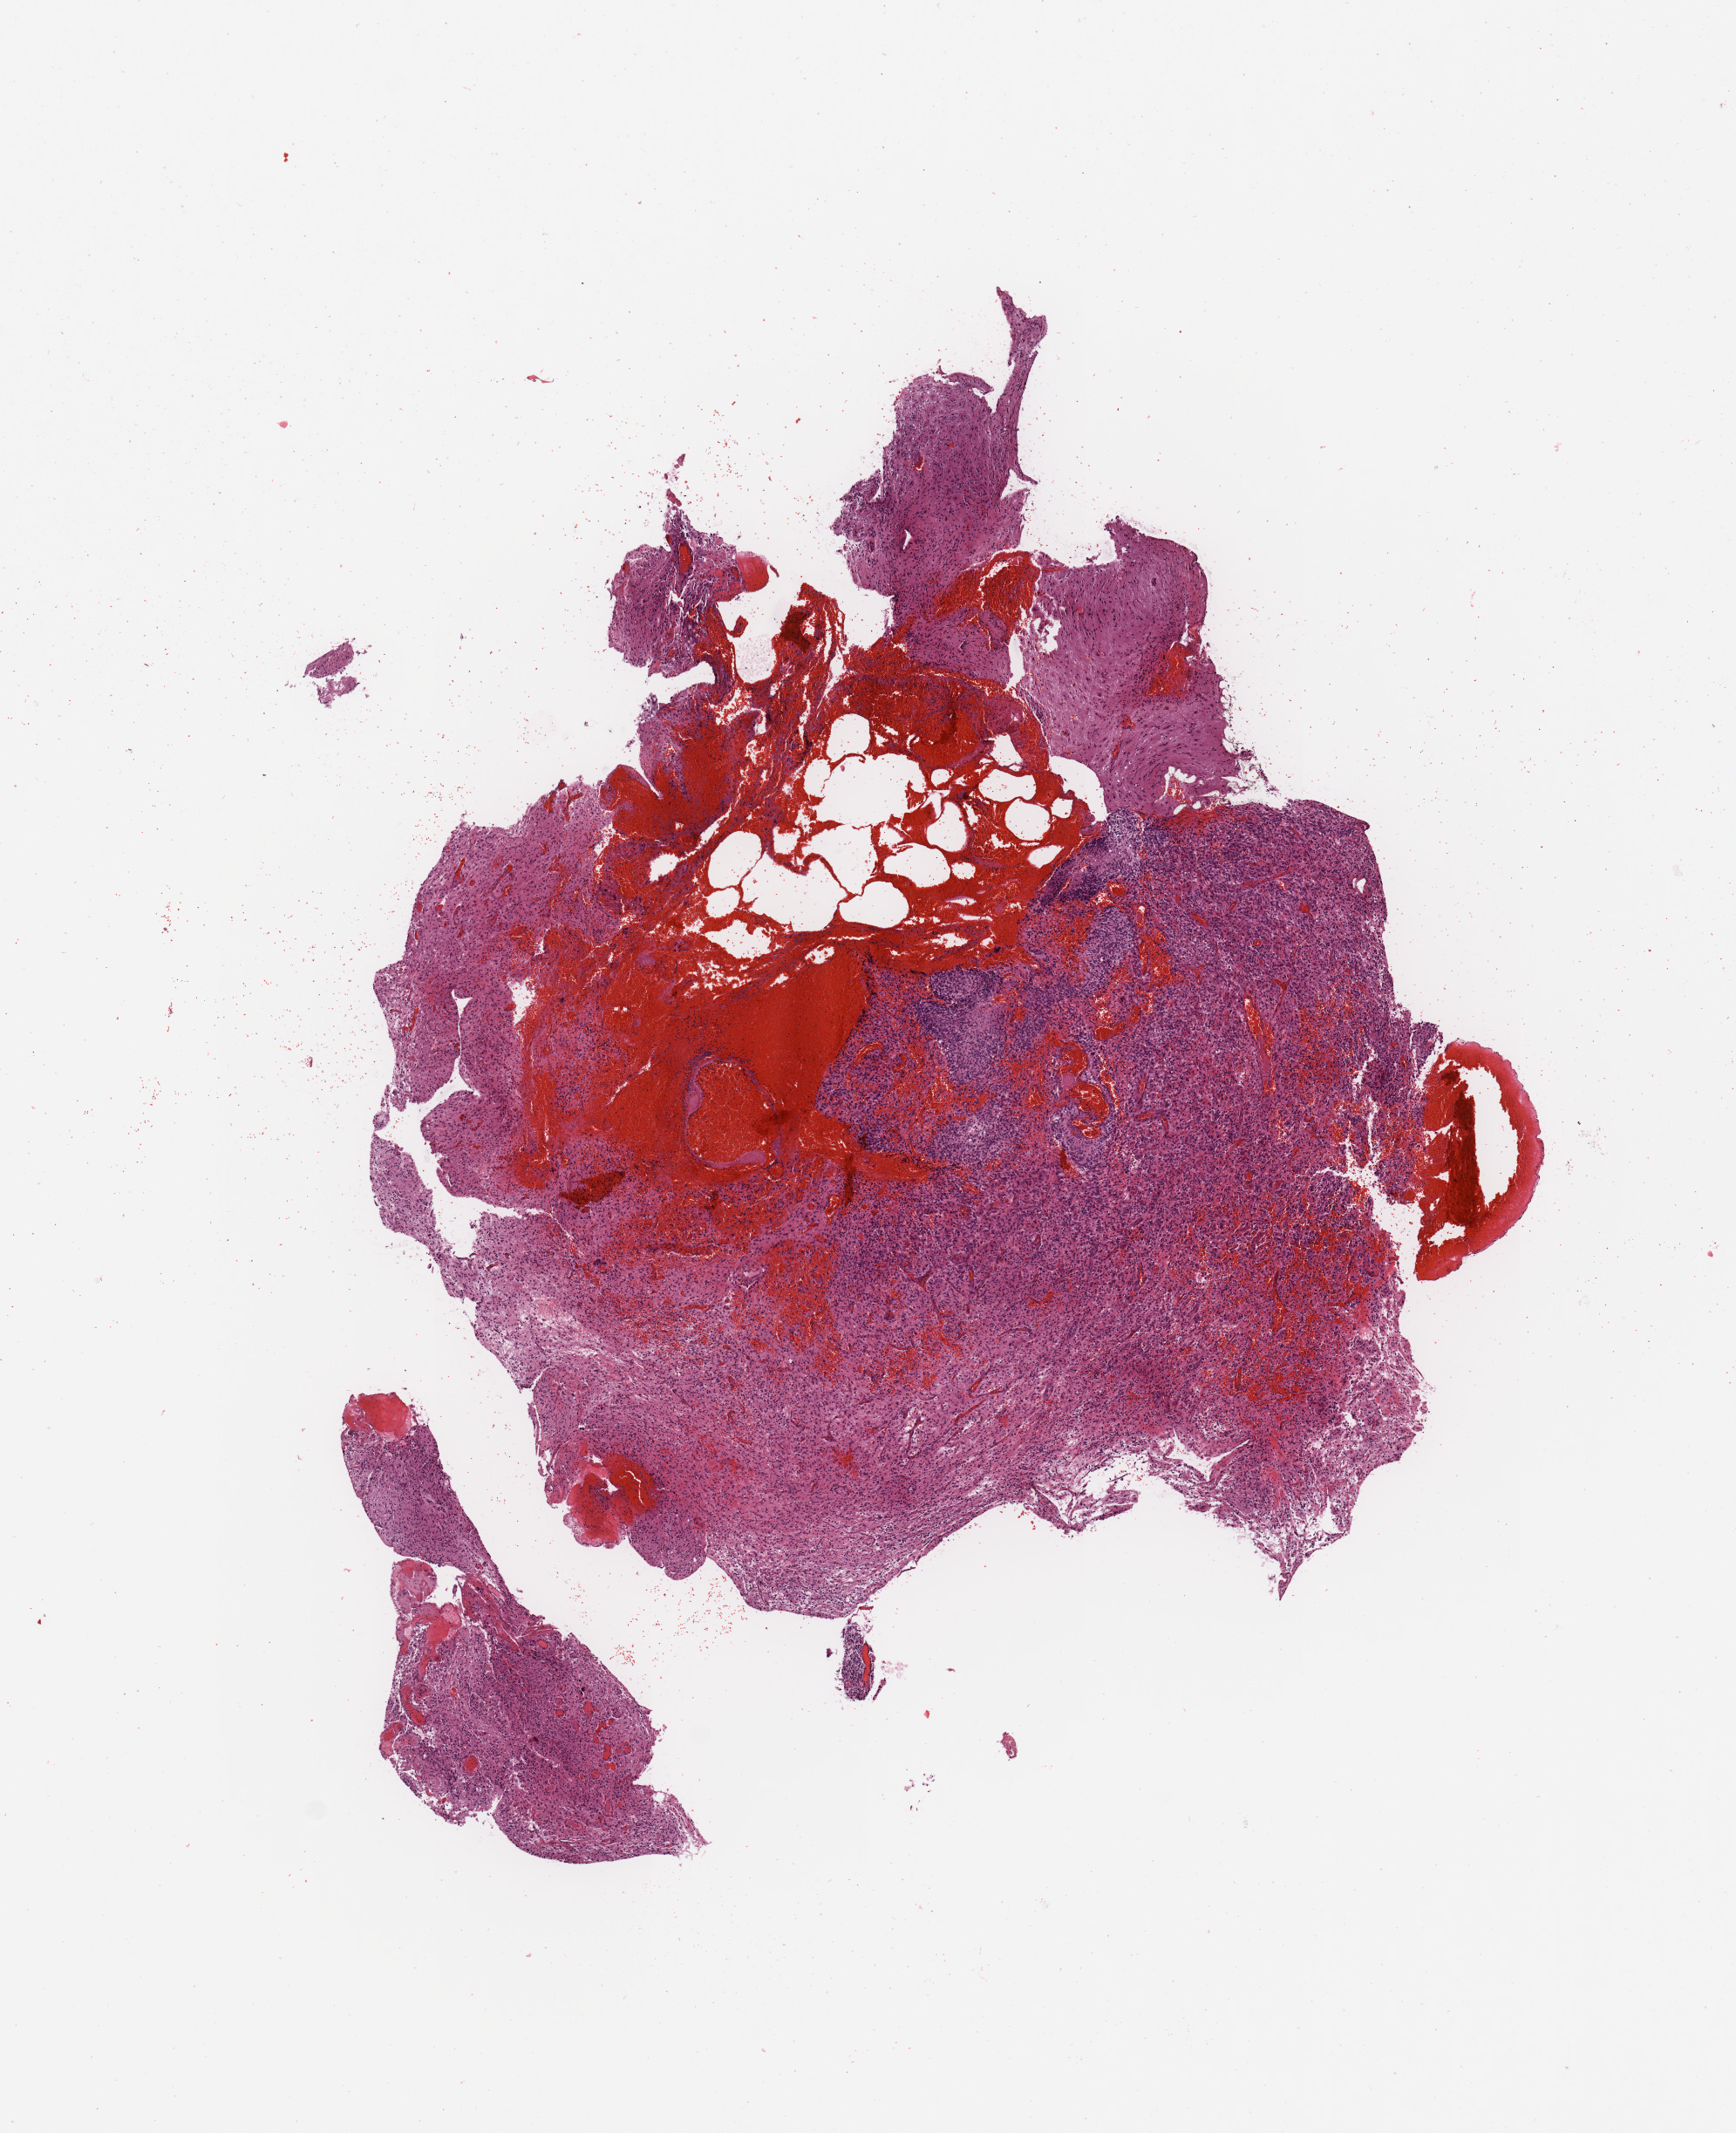
Whole-slide histology image, Hematoxylin and eosin (H&E) stained, shown as a low-resolution overview of the whole scanned area (about 7.9 x 9.7 mm), tumour tissue sample, sampled site: brain. Male, 77 y/o. Slide review estimates, as recorded: tumour nuclei 85%, necrosis 5%.
• diagnosis: Glioblastoma
• primary tumour site (as recorded): parietal lobe